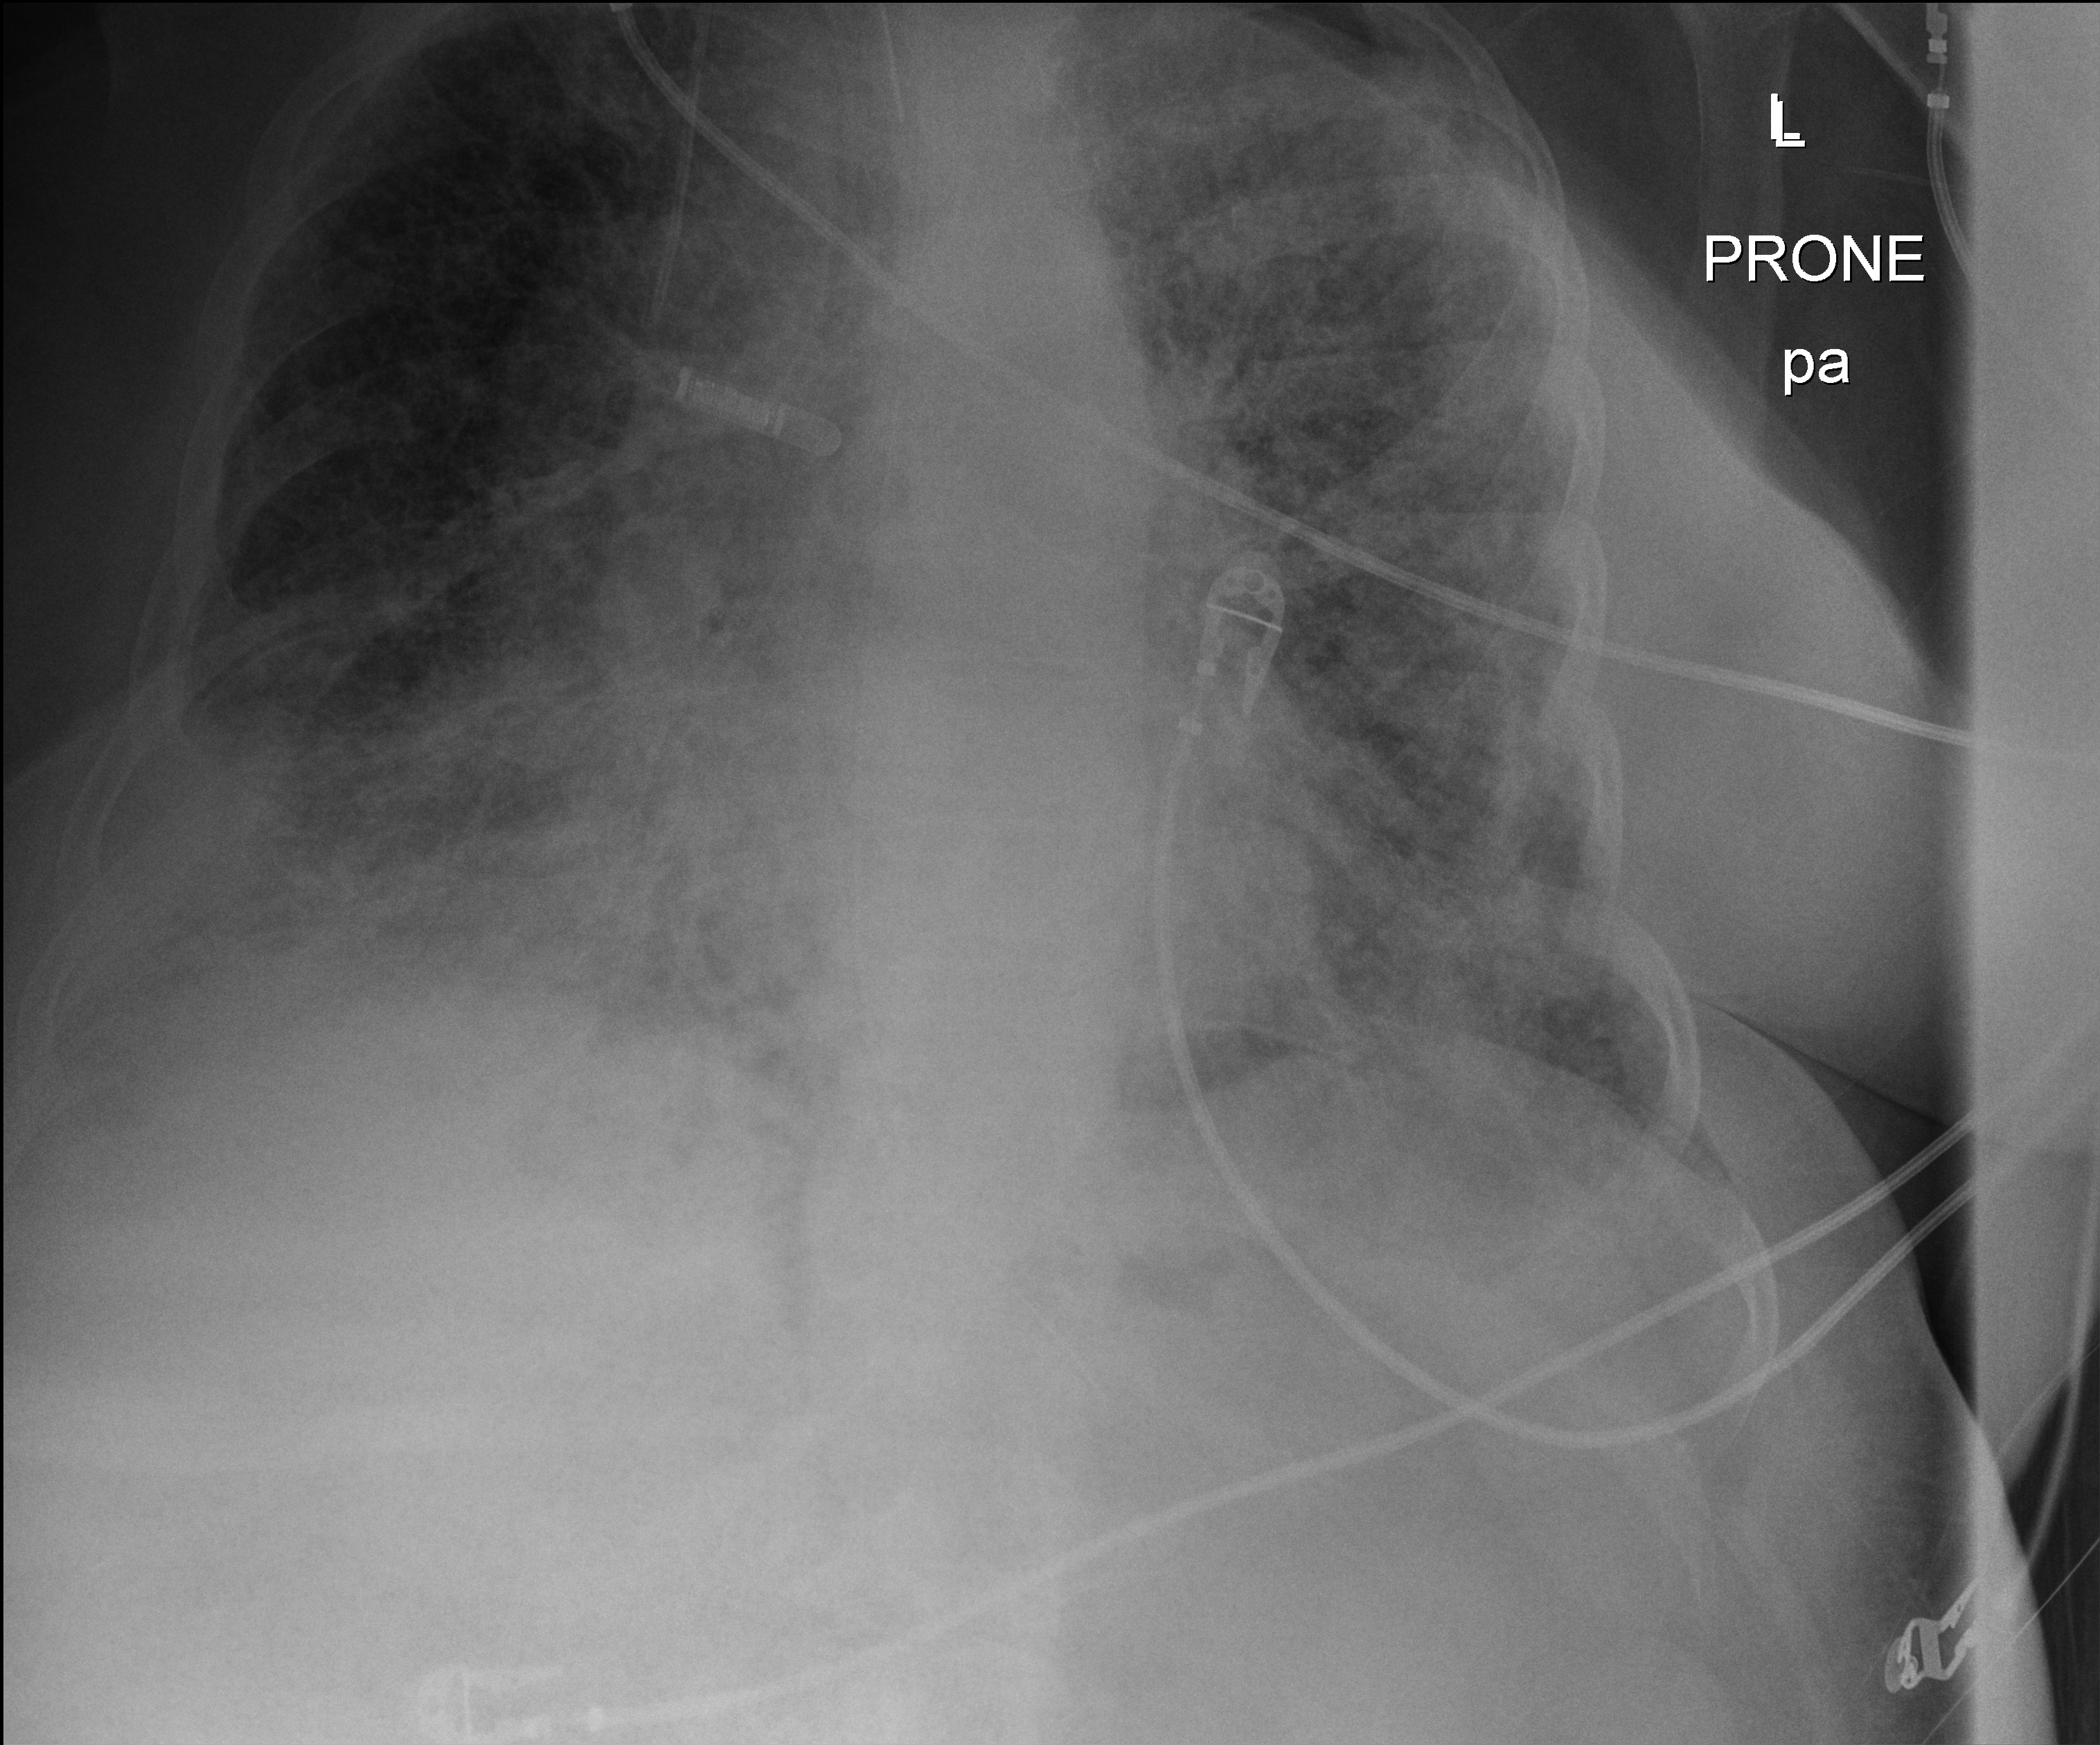
Chest X-ray (portable). Female patient hospitalised with COVID-19, age 60–74 years.
From the hospital-stay record, not from the radiograph (when in the stay this image was taken is not recorded): diabetes (admission record): yes; mechanically ventilated during this hospital stay: yes; admitted to intensive care during this hospital stay: yes.